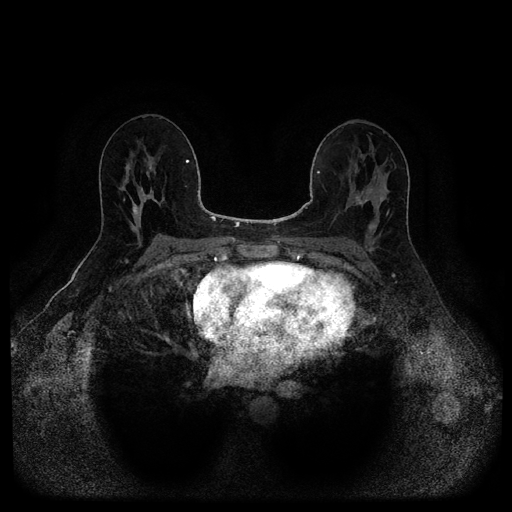
Breast MRI (dynamic contrast-enhanced, multi-phase), one axial slice. Slice 60 of 116 in the series (ordered by position). Dynamic contrast-enhanced series, time point 2 of 5 at this slice position (early post-contrast). 1.5 T. TE 2.6 ms, TR 5.3 ms. 512 × 512 image matrix, field of view 350 × 350 mm. Patient: female, 49 years.
Annotated regions visible in this slice (semi-automatic segmentation, software-assisted and operator-edited):
- breast lesion (labelled benign in the annotation): bounding box [x1, y1, x2, y2] px = [368, 223, 377, 233]